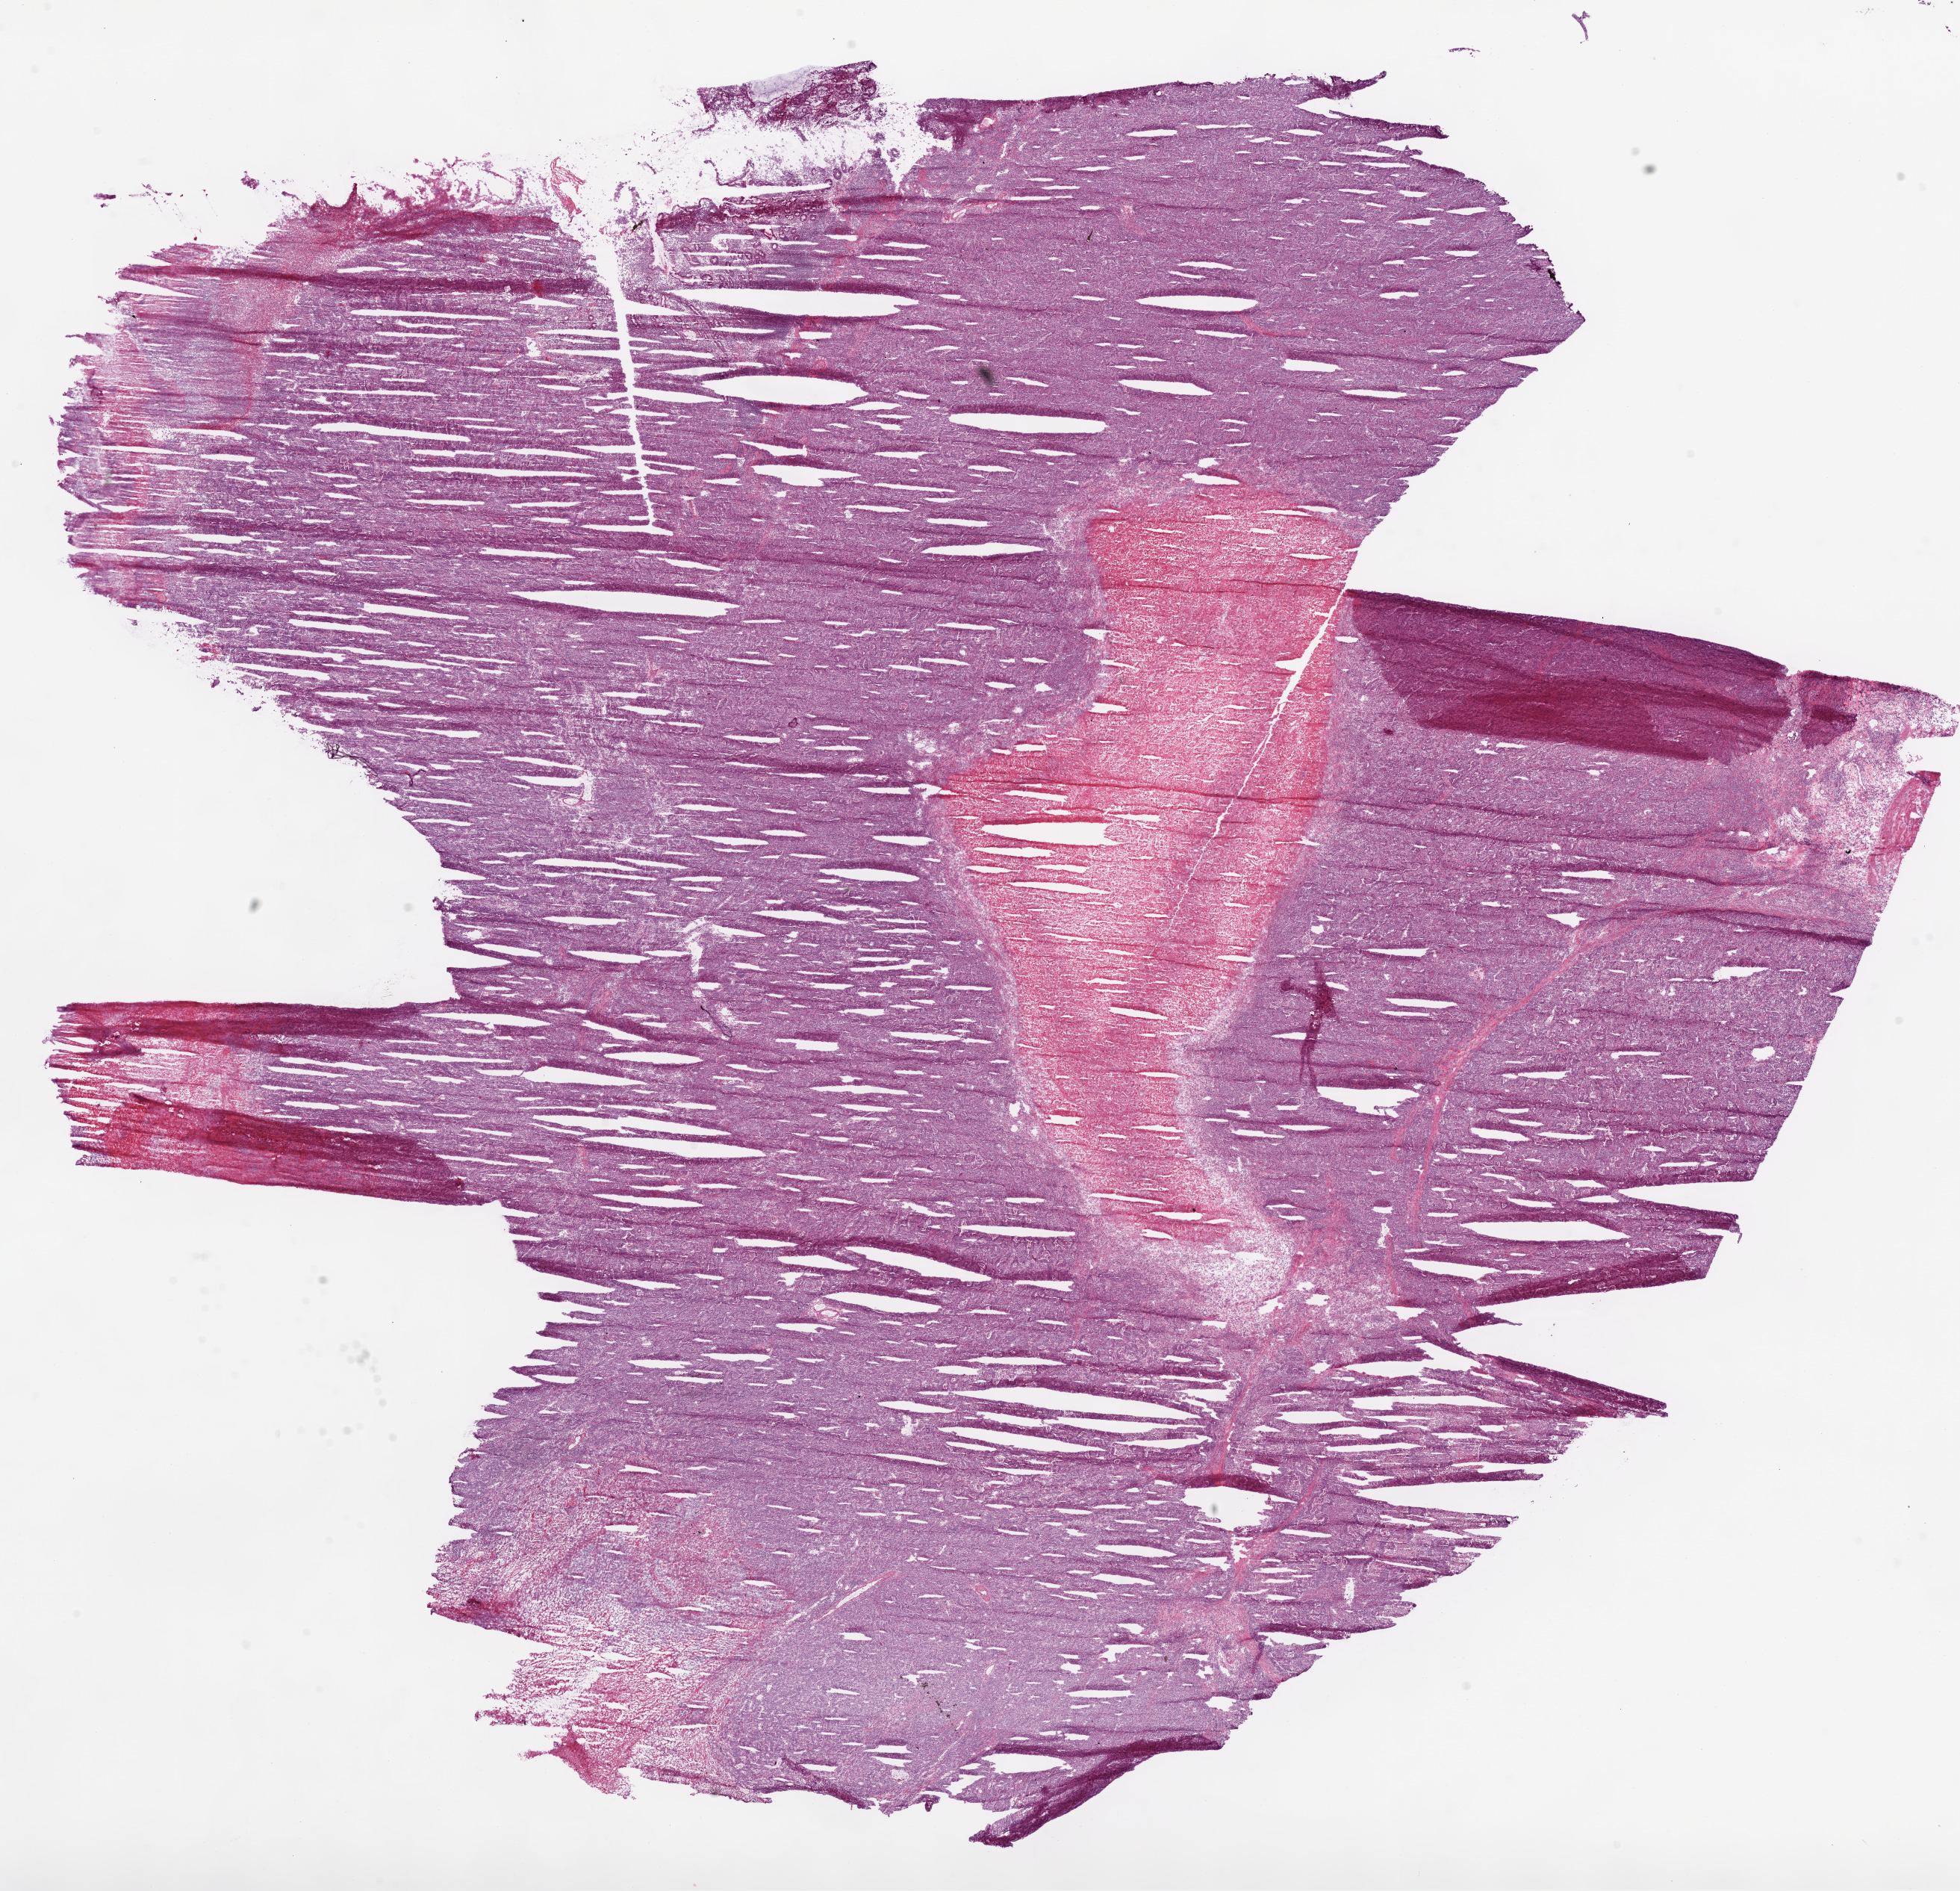
Digitized H&E tissue section (whole slide) — a low-resolution overview of the entire scanned area, about 21.1 x 20.3 mm (acquisition: 20x scan), frozen section from the top of the tissue portion, primary tumour sample from the stomach. Female, age 80 years at initial diagnosis. Histologic grade: G3 (poorly differentiated). Pathologist review of this section (percent, as recorded): tumour cells 67%, tumour nuclei 70%, normal cells 5%, stromal cells 10%, necrosis 18%.
* diagnosis: Adenocarcinoma, NOS
* lymph nodes positive (case pathology): 3 of 8 examined
* AJCC pathologic stage: IIIA